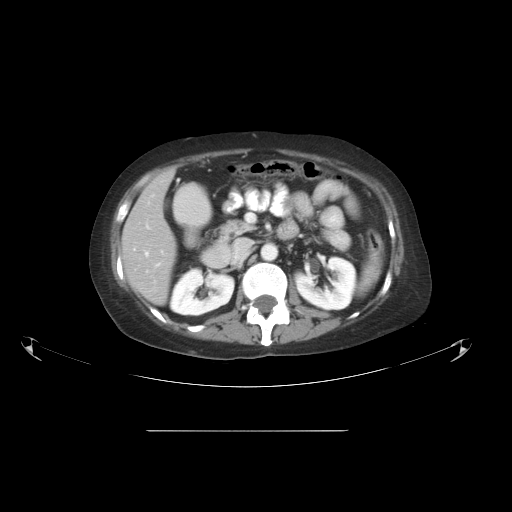
Contrast-enhanced abdominal CT, one axial slice. Slice 26 of 51 in the series (ordered by position). 120 kVp. Intravenous contrast given. Soft-tissue window (W 400 / L 40 HU). 5 mm slice thickness. 512 × 512 image matrix. Female patient, age 48 years. From the clinical record (not read from this slice): diagnosis: colorectal cancer liver metastases, imaged before liver resection; multiple liver metastases: yes; largest metastasis: 1 cm; chemotherapy before resection: no.
Structures marked on this image (manually delineated by an expert):
- hepatic veins: box from (x=145, y=252) to (x=159, y=266) px
- liver: (x=122, y=172)–(x=176, y=305)
- planned liver remnant (the part of the liver to remain after resection): (x=122, y=172)–(x=176, y=305)
- portal vein (with intrahepatic branches): (x=134, y=226)–(x=150, y=250)